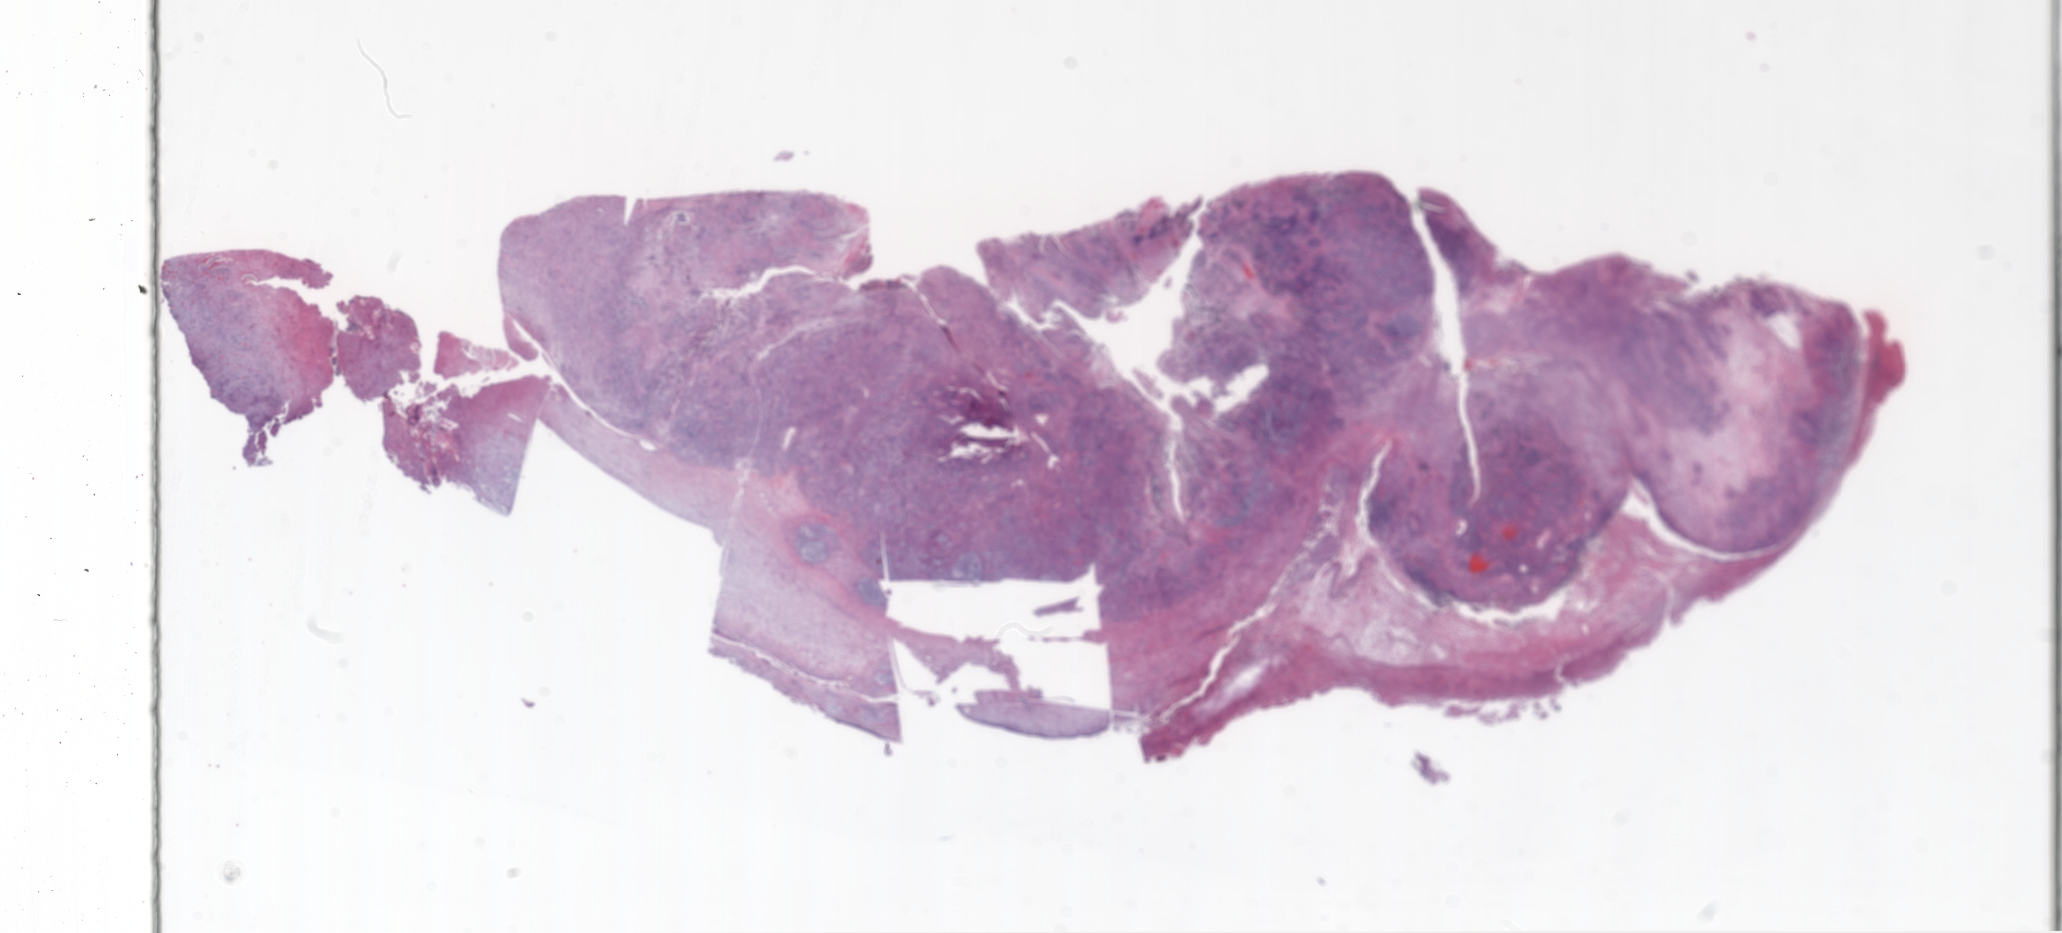
Whole-slide histology image, Hematoxylin and eosin (H&E) stained, a low-resolution overview of the entire scanned area, about 33.1 x 15.0 mm (acquisition: 20x scan). Formalin-fixed paraffin-embedded (FFPE) diagnostic section. Sample: primary tumour, brain. Male patient; age at initial diagnosis 42 years.
* diagnosis: Glioblastoma